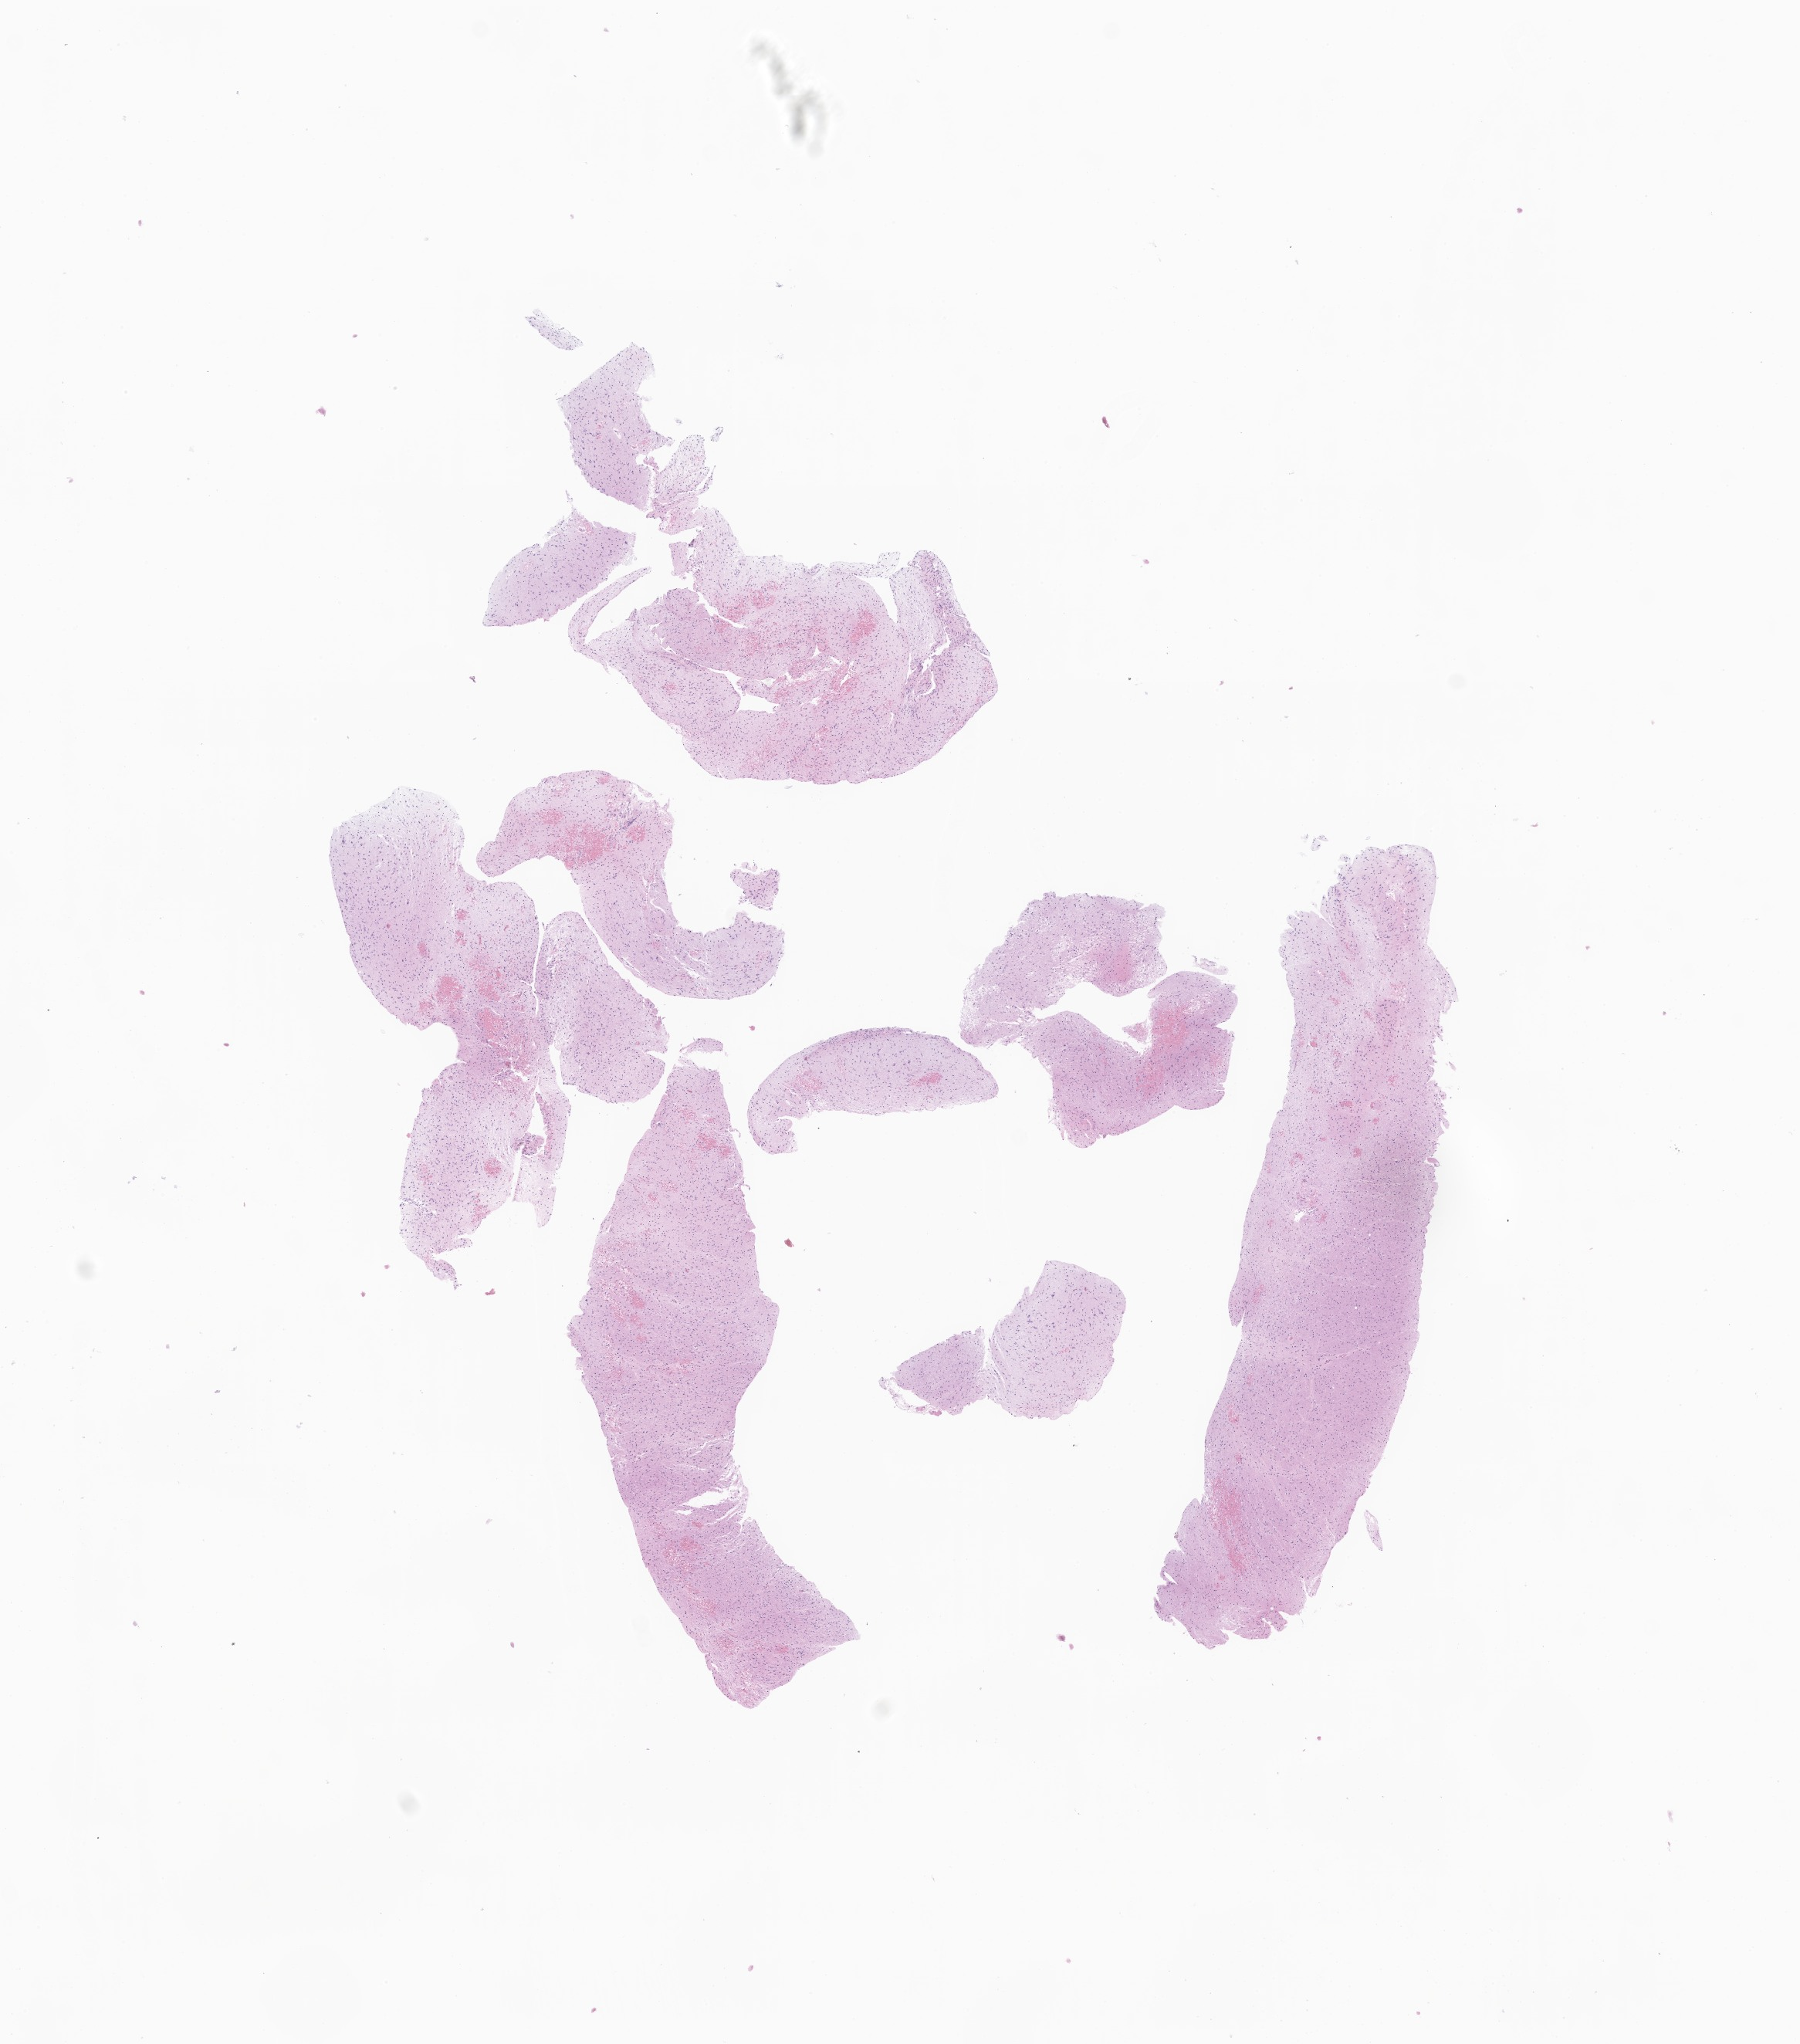
Digitized hematoxylin and eosin (H&E)-stained section of tumor tissue from the brain, low-resolution overview of the scanned area, about 9.8 x 11.2 mm. Formalin-fixed paraffin-embedded section. Patient: female, age 113 months (9 years 5 months).
Diagnosis: Neoplasm, uncertain whether benign or malignant.